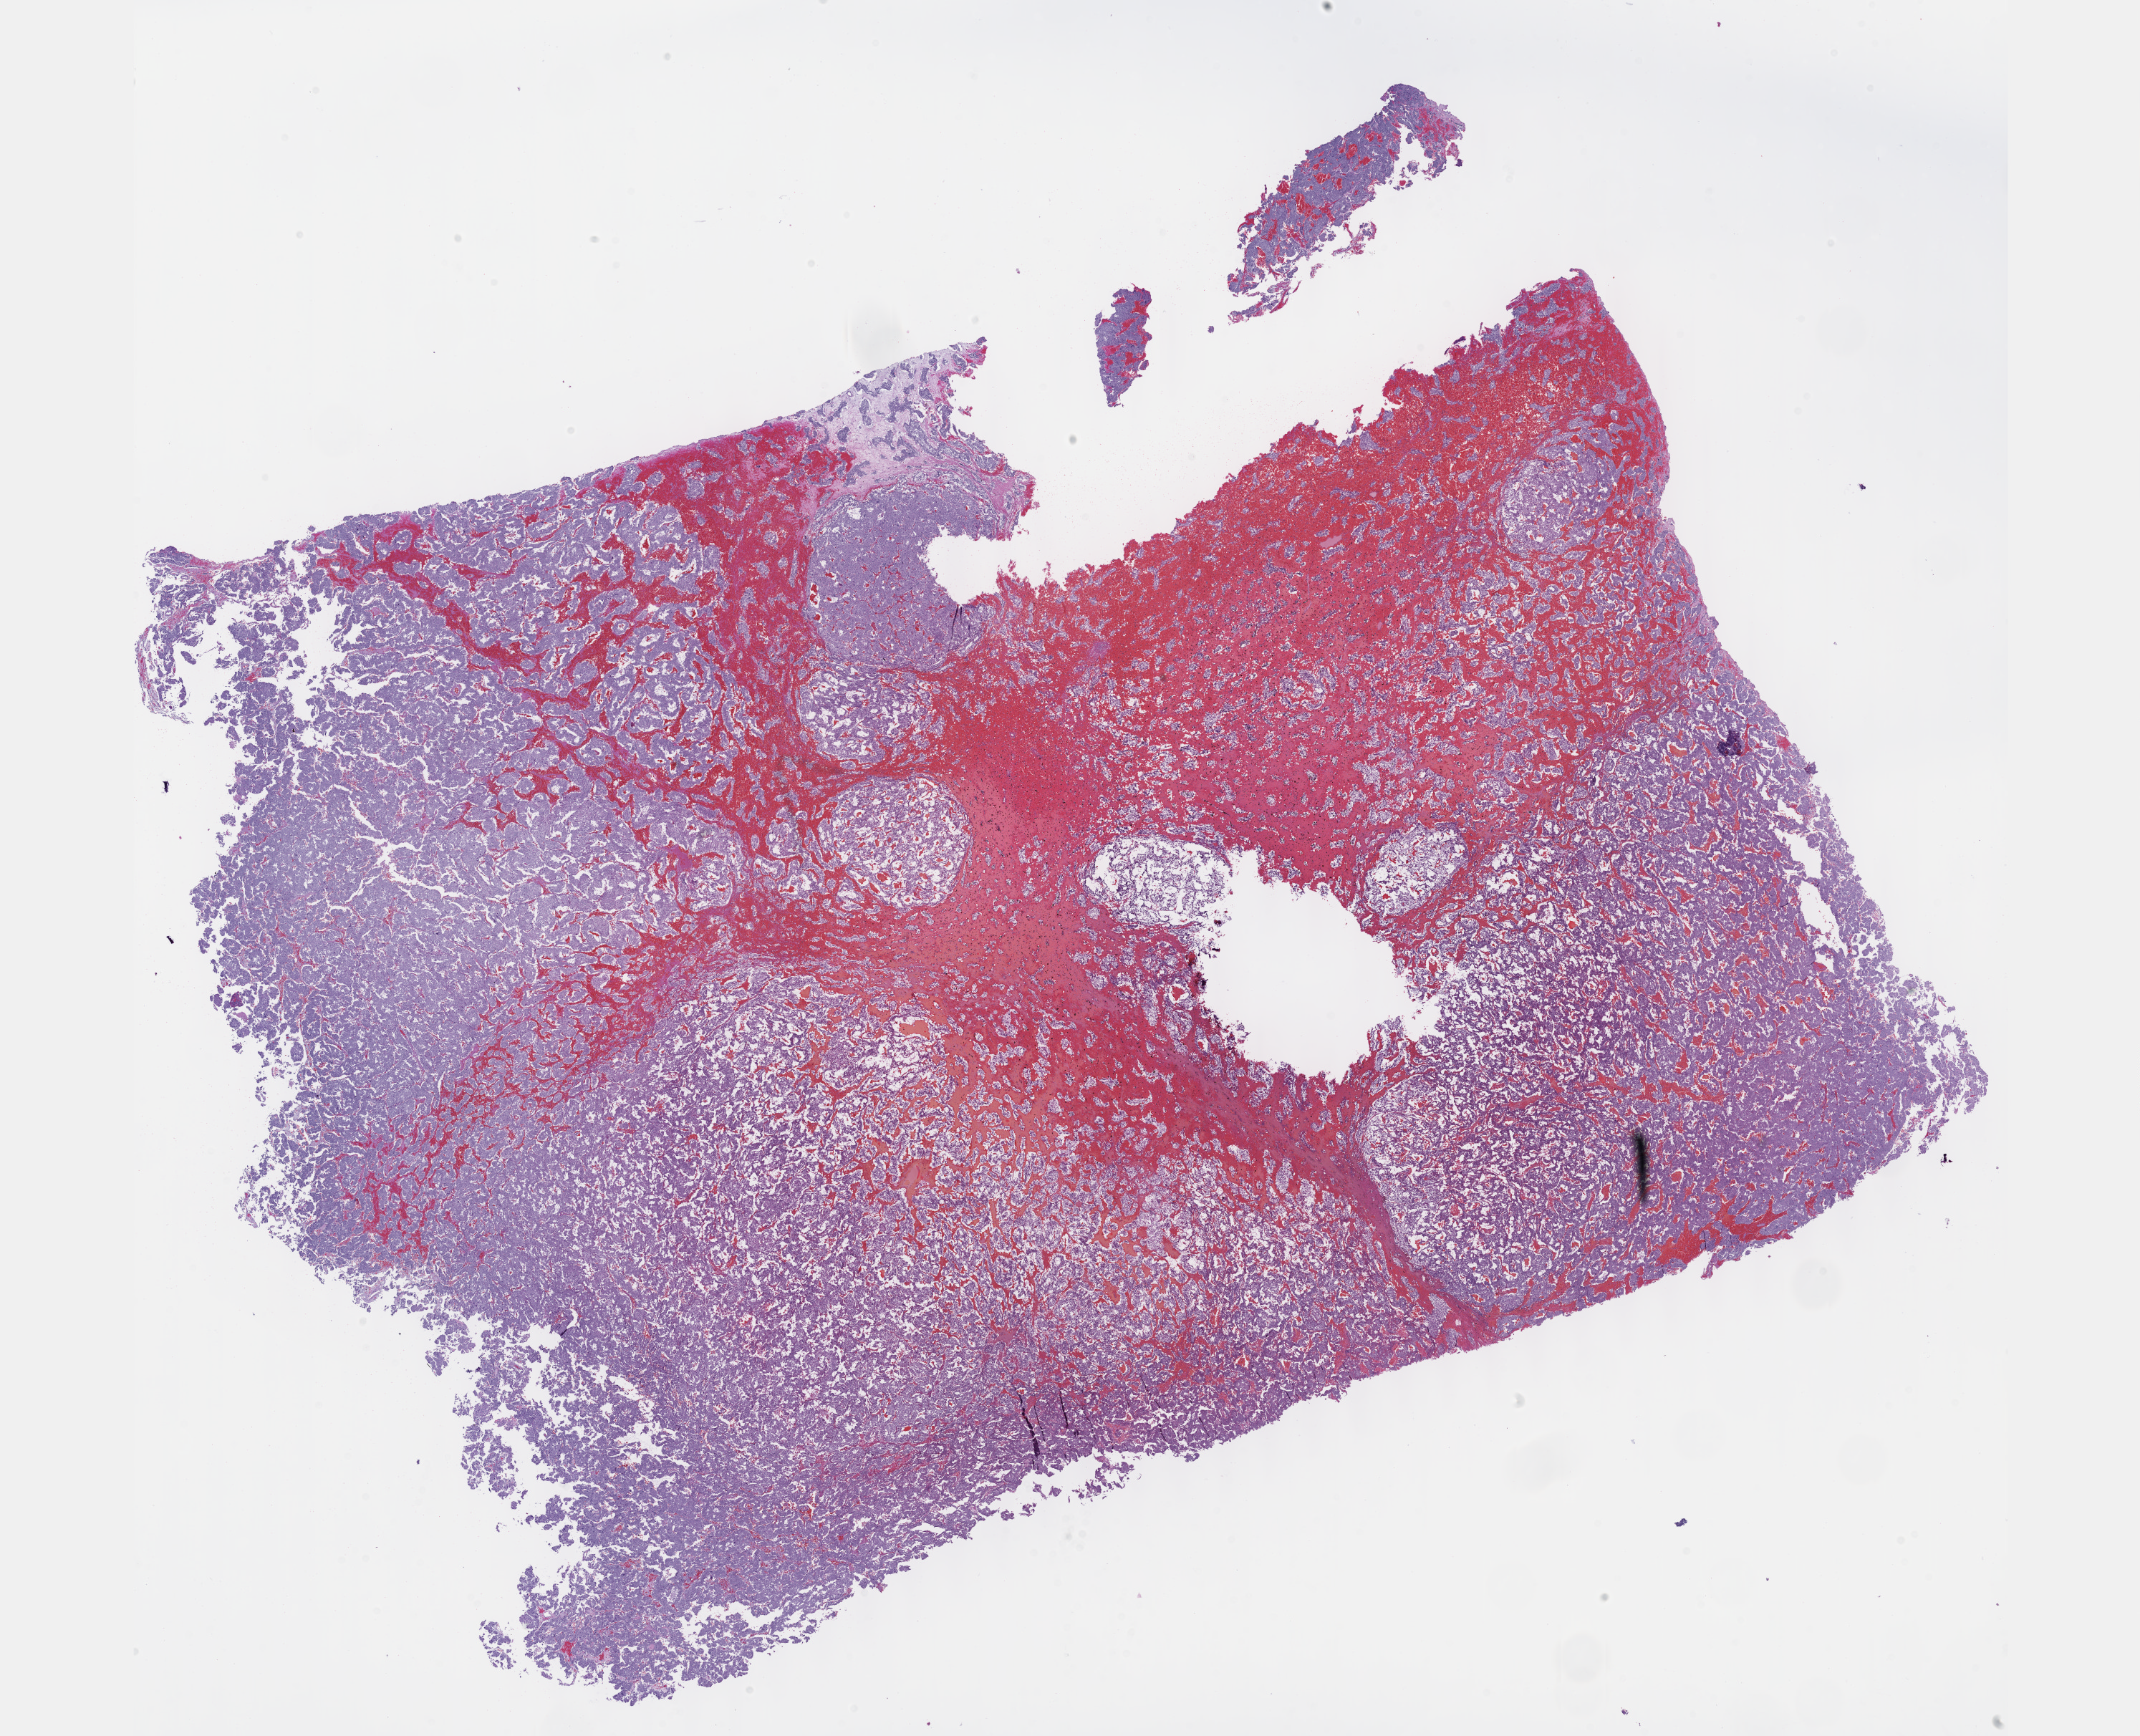
Whole-slide histology image, Hematoxylin and eosin (H&E) stained, a low-resolution overview of the entire scanned area, about 24.1 x 19.6 mm (slide scanned at 40x). Formalin-fixed paraffin-embedded (FFPE) diagnostic section. Primary tumour sample from the adrenal gland. Male patient; age at initial diagnosis 61 years.
Pathologic diagnosis: Pheochromocytoma, NOS.